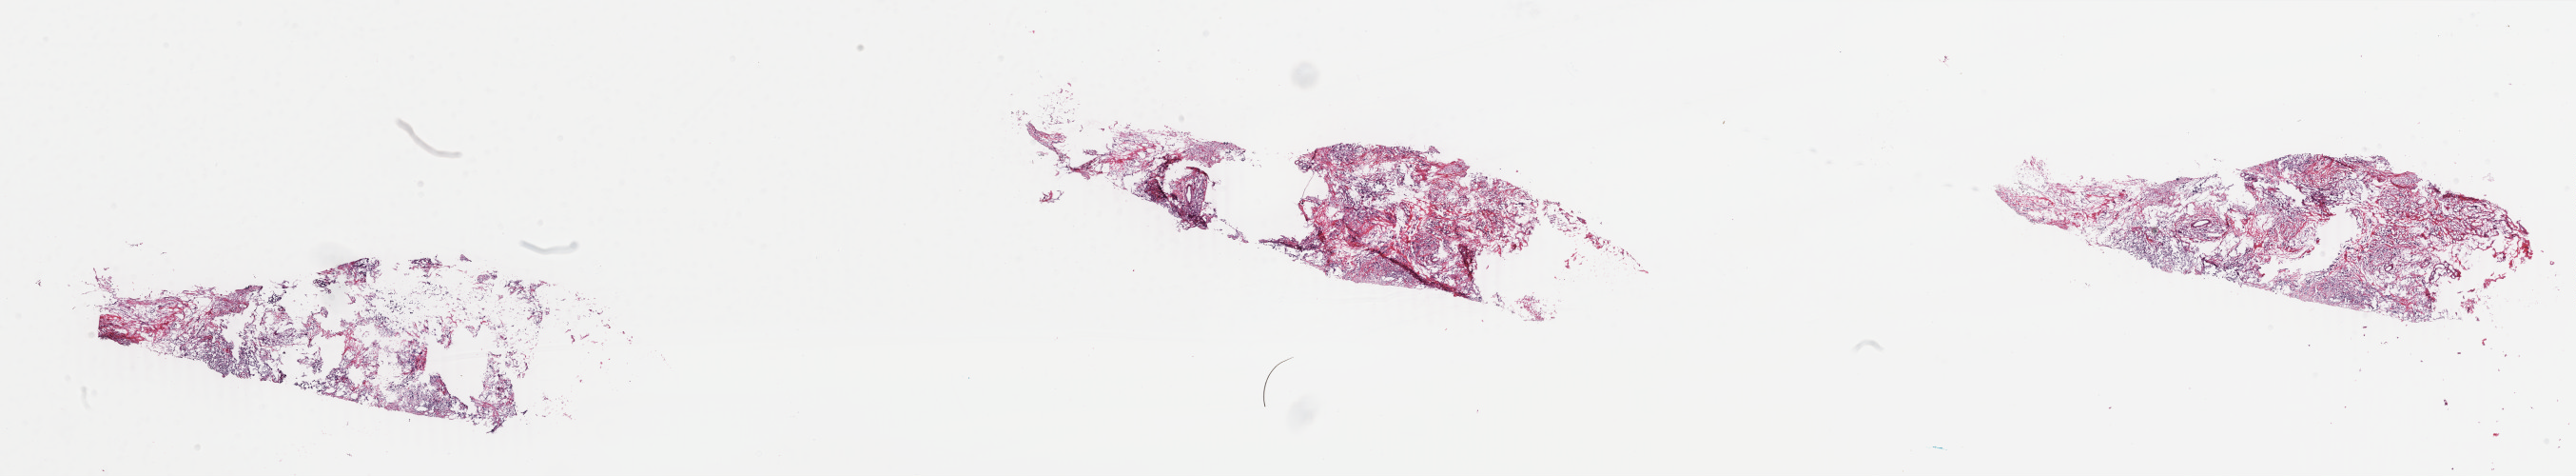
Digitized H&E tissue section (whole slide) — whole scanned area (about 43.1 x 8.0 mm, from a 40x scan) shown as a low-resolution overview; frozen section; primary tumour sample from the breast. Female, age 62 years at initial diagnosis. Pathologist review of this section (percent, as recorded): tumour cells 100%, tumour nuclei 70%.
Diagnosis: Infiltrating duct carcinoma, NOS.